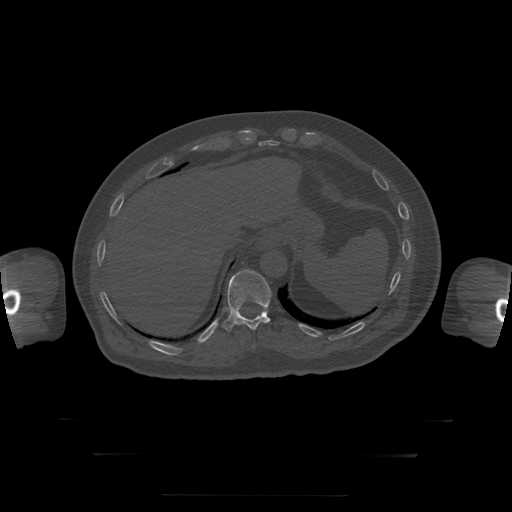
CT including the spine, one axial slice. Position 101 of 397 along the scan axis. Reconstruction kernel STANDARD. 120 kVp. Bone window (W 1800 / L 400 HU). 512 × 512 image matrix, field of view 510 × 510 mm. Patient age 73 years. Case-level facts recorded for this patient, not image findings: primary cancer: prostate.
Outlined on this slice (semi-automatically segmented with operator editing):
- T11 vertebra: bounding box (x1, y1, x2, y2) in pixels: (222, 270, 271, 332)